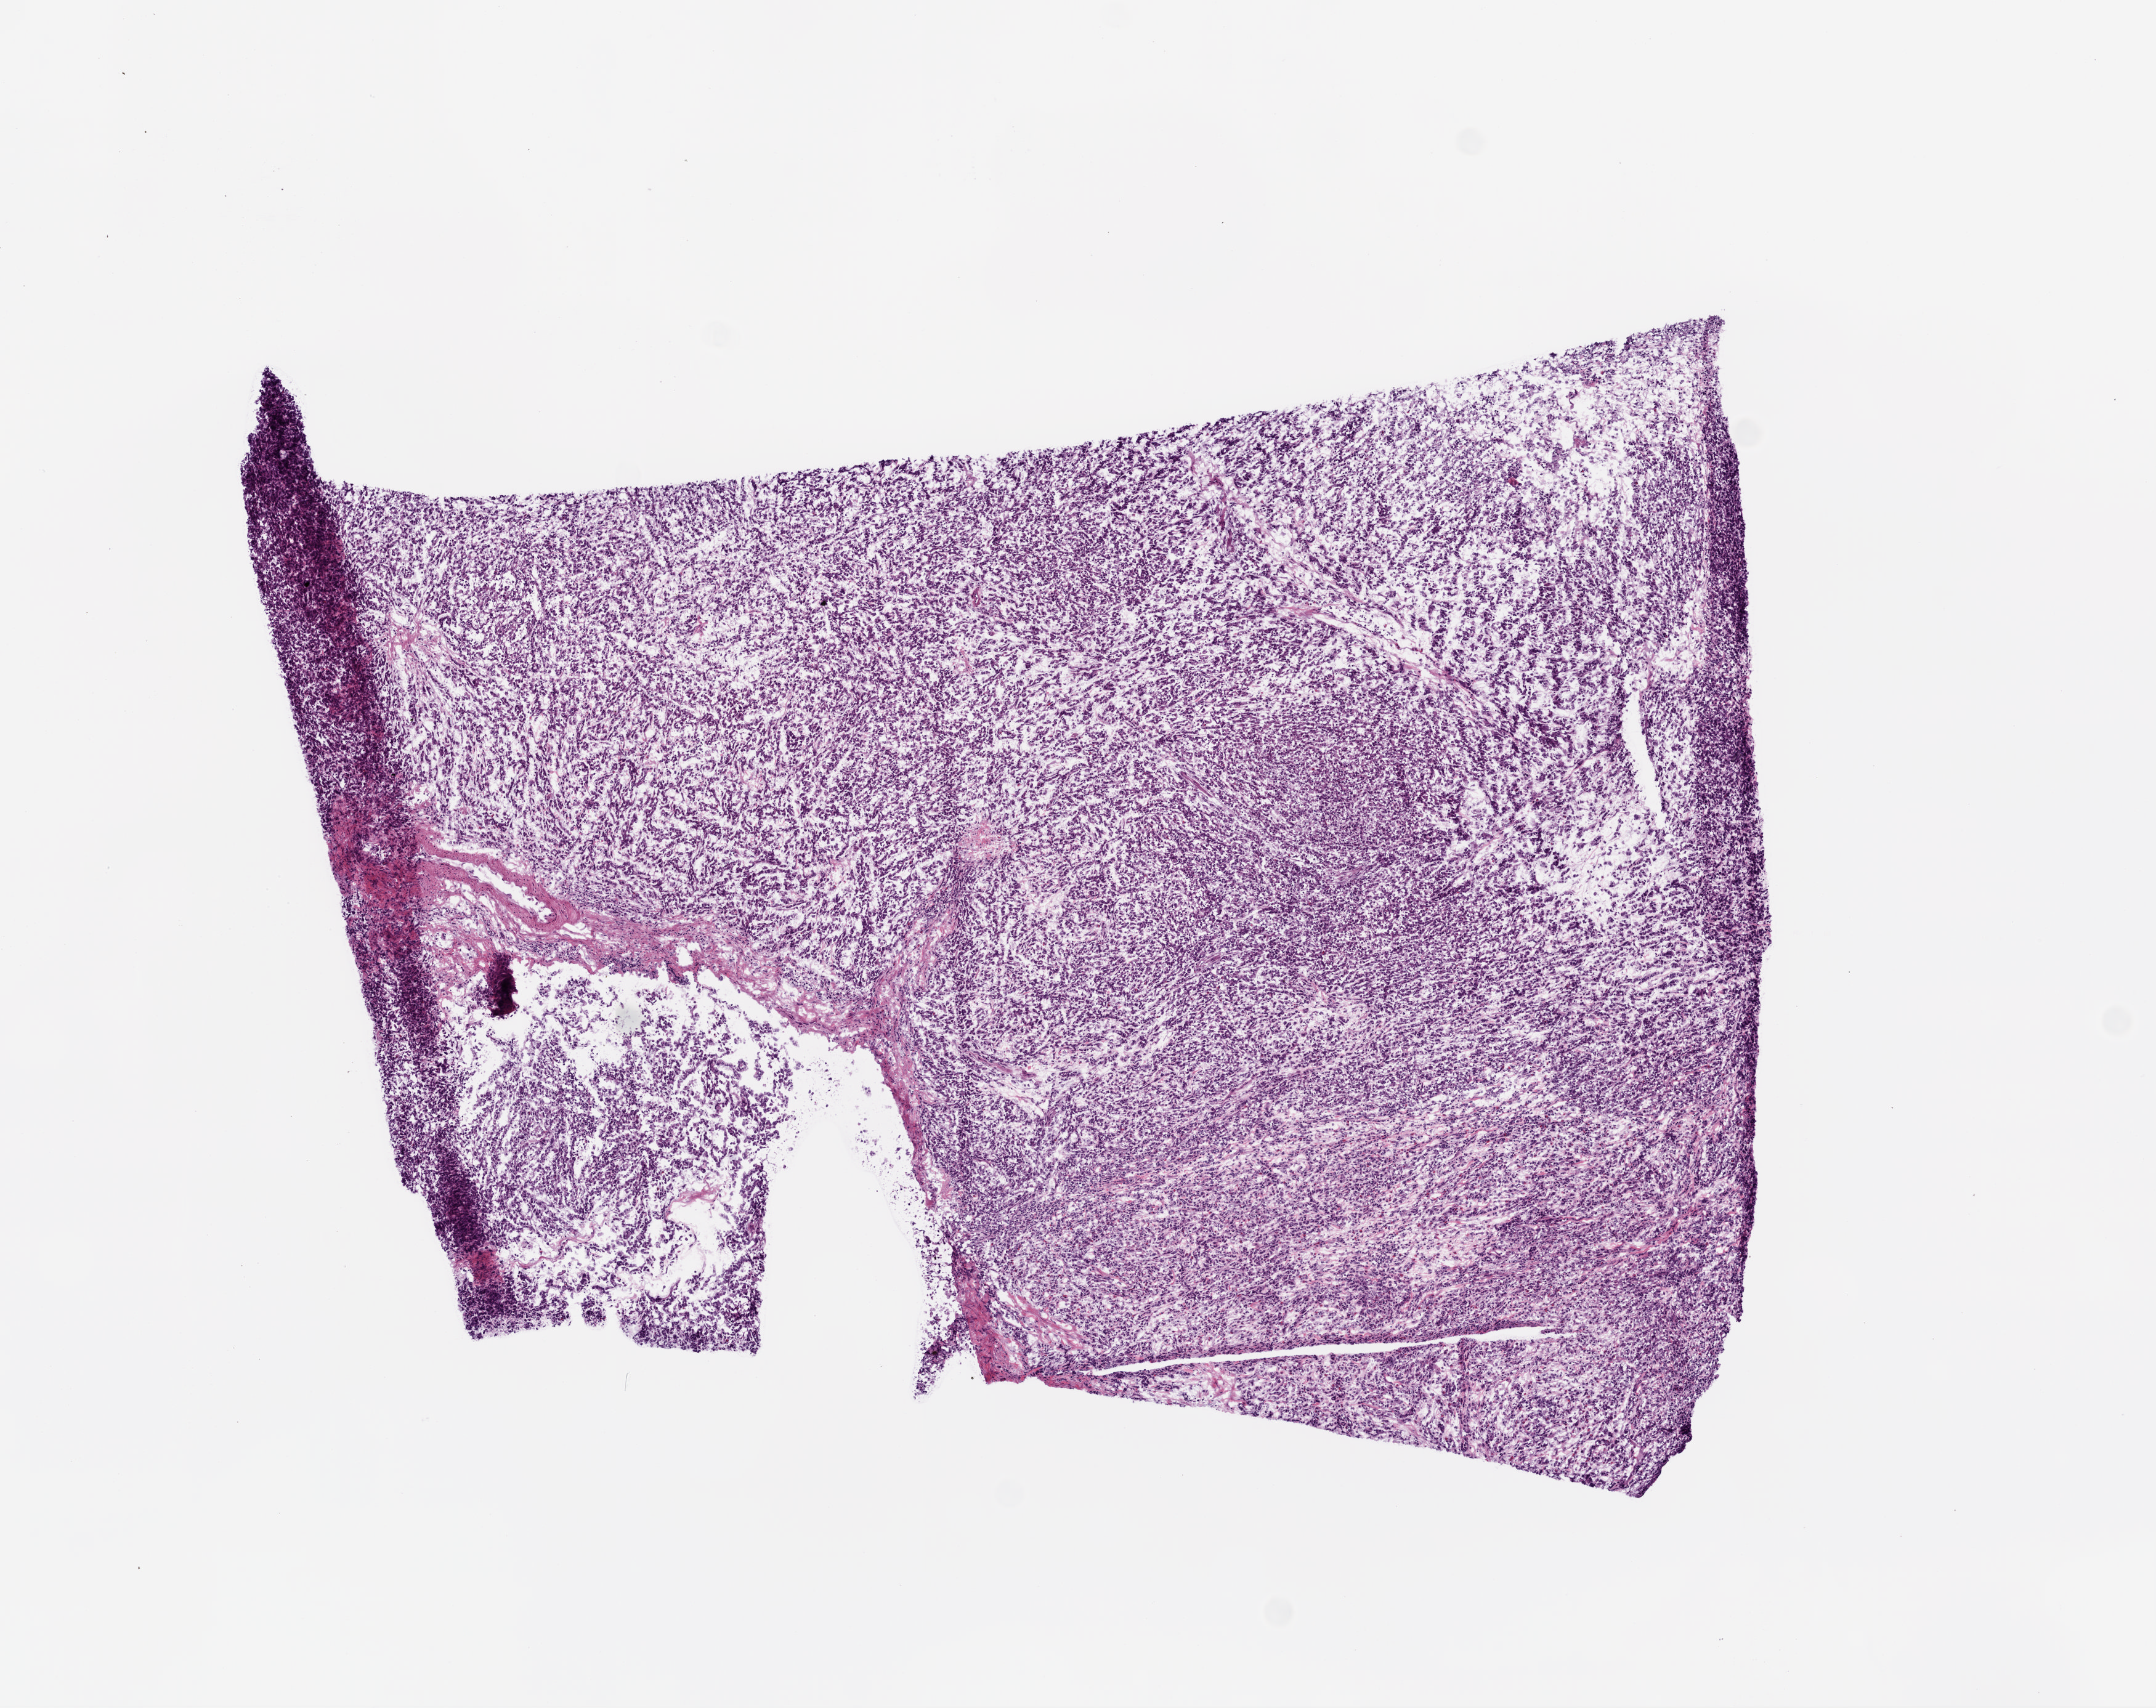
Digitized H&E tissue section (whole slide), low-resolution overview of the scanned area, about 7.0 x 5.6 mm (acquisition: 20x scan), frozen section from the bottom of the tissue portion, primary tumour sample from the stomach. Male patient; age at initial diagnosis 71 years. Histologic grade: G3 (poorly differentiated). Pathologist review of this section (percent, as recorded): tumour cells 88%, tumour nuclei 75%, normal cells 0%, stromal cells 10%, necrosis 2%.
Lymph nodes positive (case pathology): 0 of 60 examined. AJCC pathologic stage: IB. Pathologic diagnosis: Adenocarcinoma, NOS (cardia, NOS).